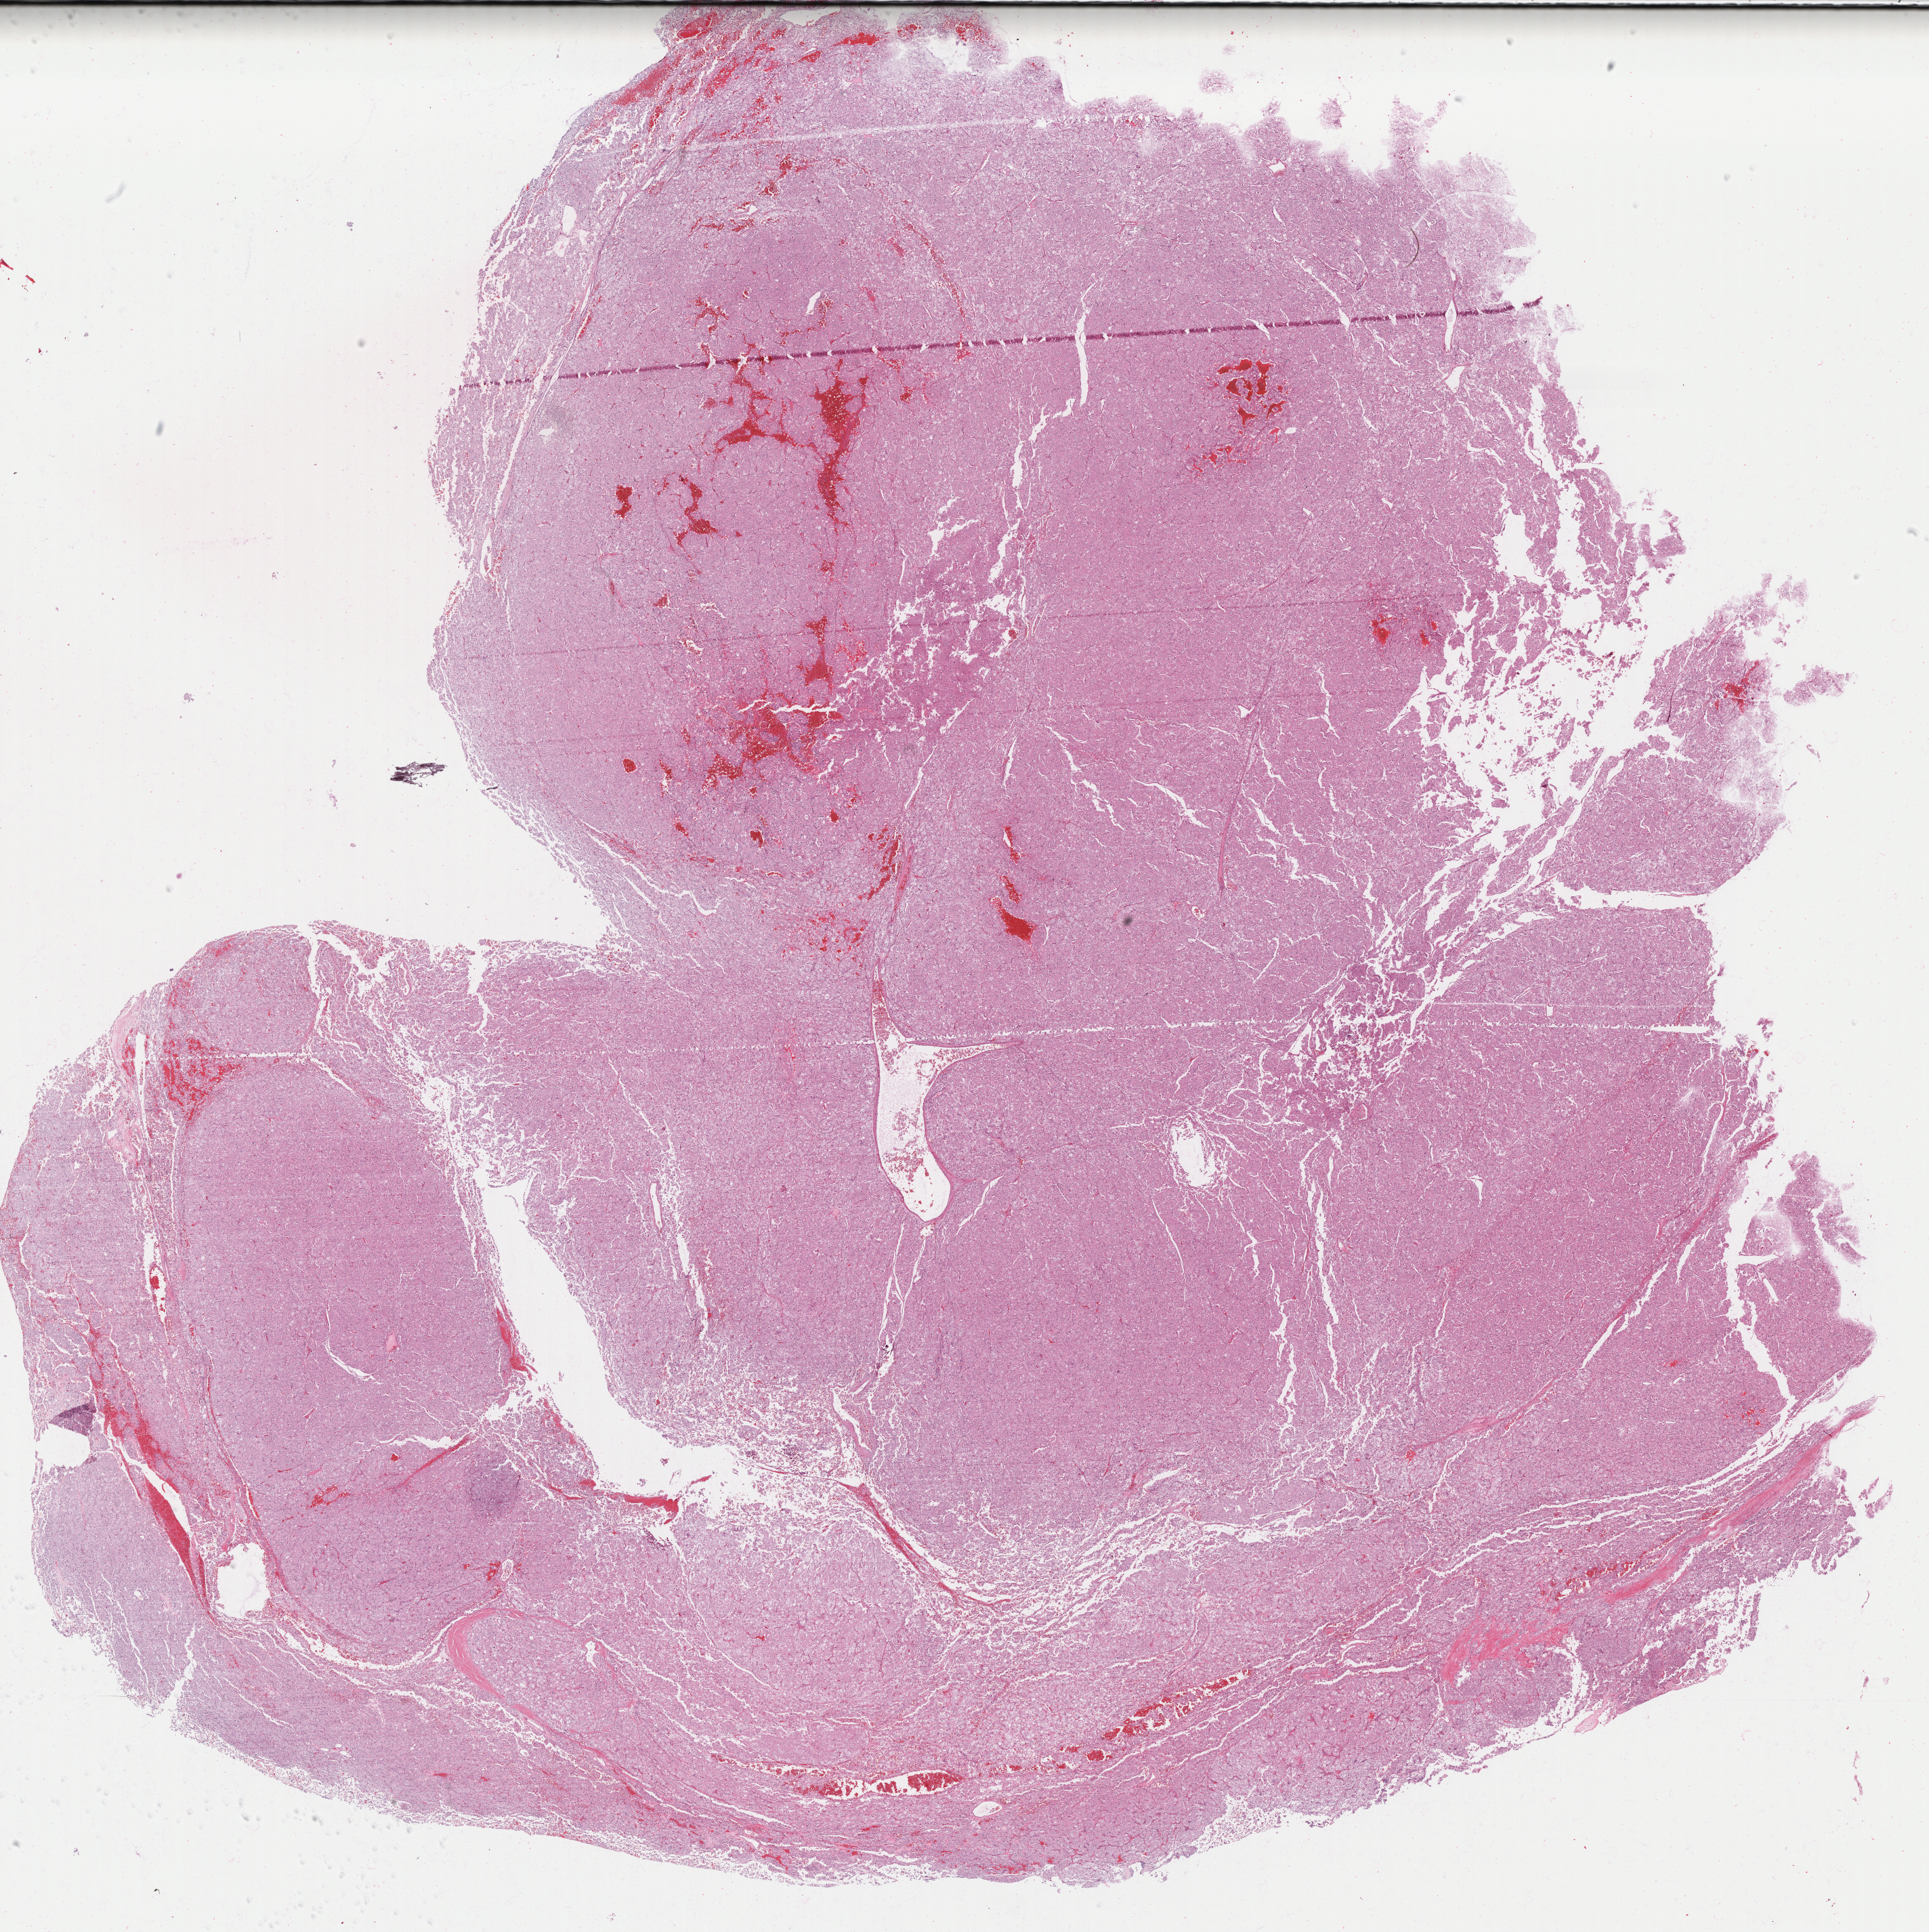
Digitized H&E-stained tissue section (whole slide), whole scanned area (about 23.0 x 23.0 mm) shown as a low-resolution overview. Formalin-fixed paraffin-embedded (FFPE) diagnostic section. Sample: primary tumour, kidney. Female patient; age at initial diagnosis 41 years.
- lymph nodes positive (case pathology): 0 of 3 examined
- histologic diagnosis: Renal cell carcinoma, chromophobe type
- TNM: T2 N0
- AJCC pathologic stage: II (5th edition)
- laterality: right